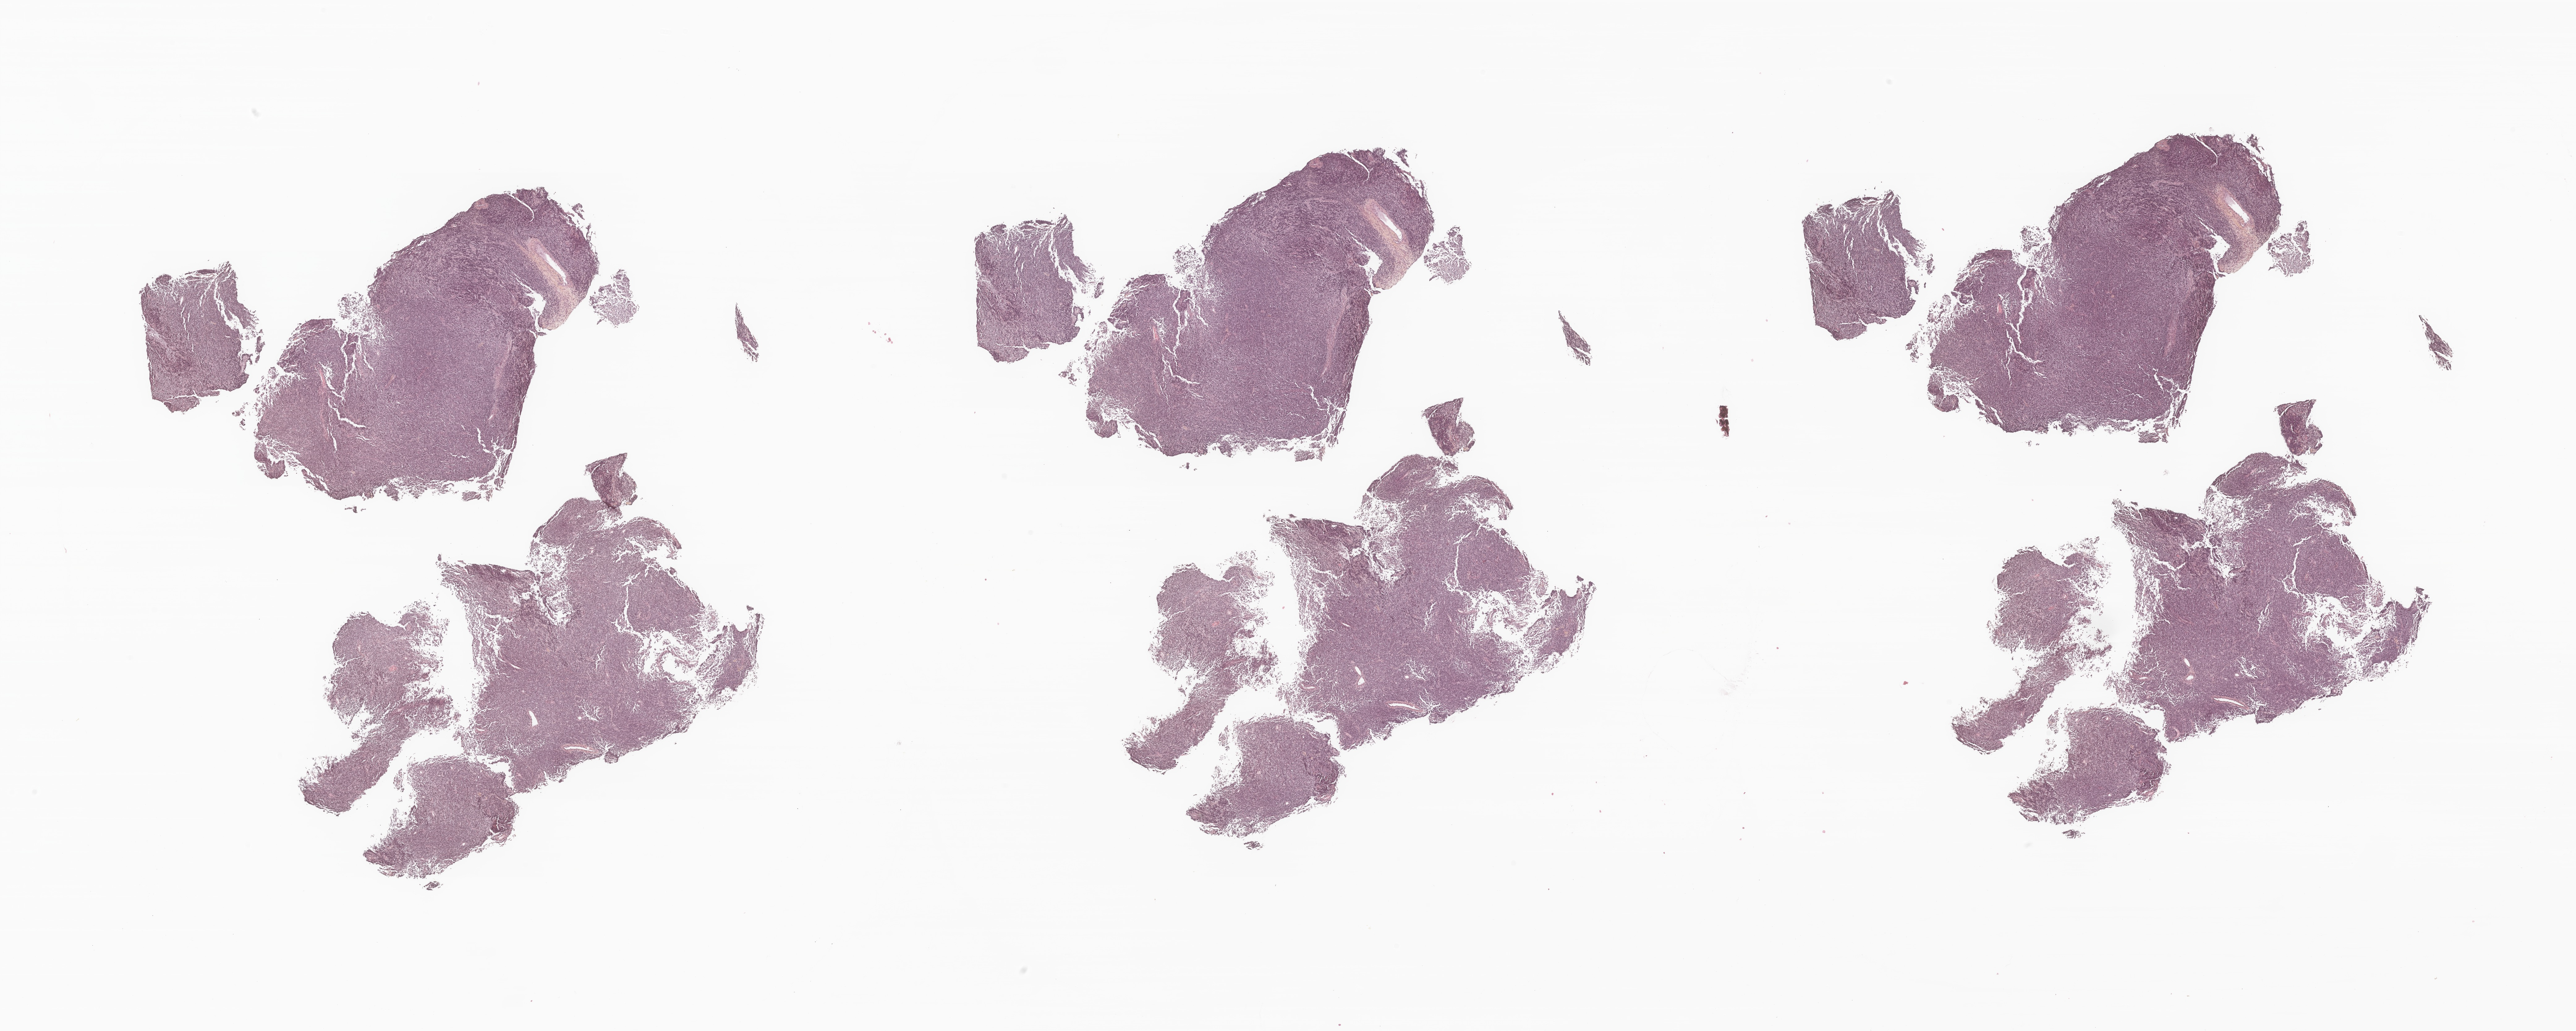
H&E whole-slide image of tumor tissue from the soft tissues of head and neck — a low-resolution overview of the entire scanned area, about 35.1 x 14.1 mm. Formalin-fixed, paraffin-embedded (FFPE) tissue. Patient: male, age 40 months (3 years 4 months).
* diagnosis (ICD-O-3 morphology term): Alveolar rhabdomyosarcoma
* tissue or organ of origin (case record): connective, subcutaneous and other soft tissues of head, face, and neck